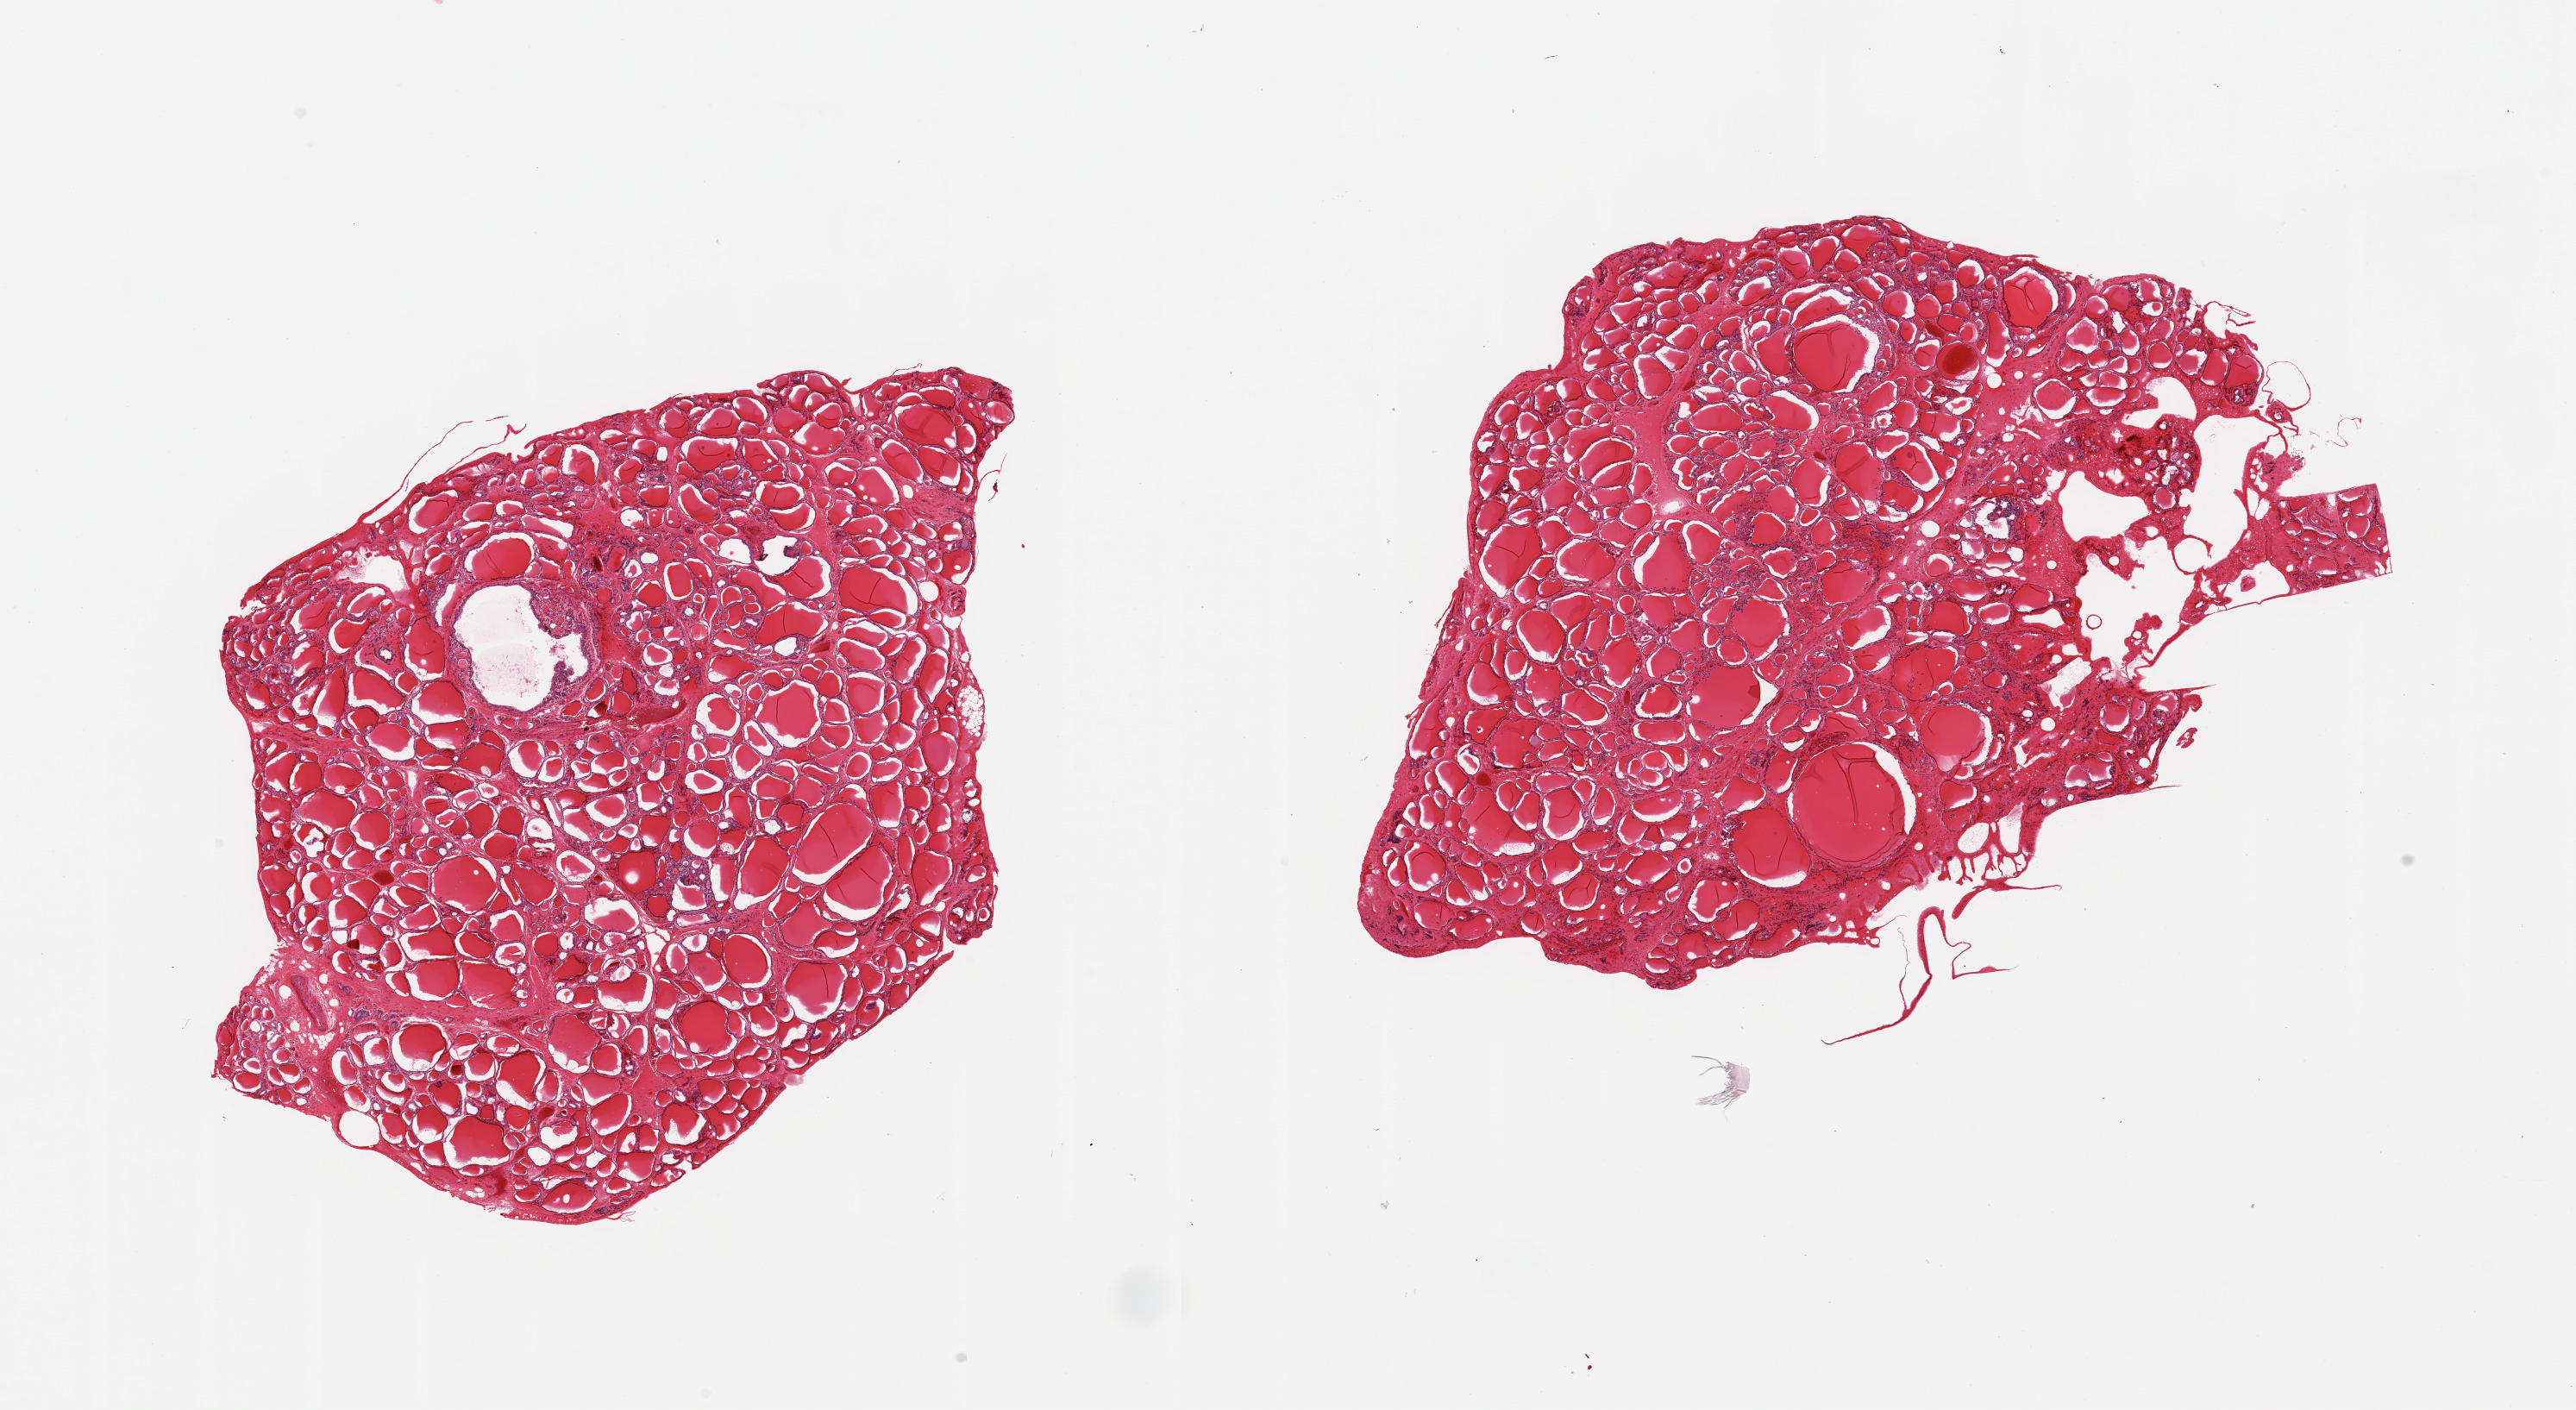
Whole-slide image, hematoxylin and eosin (H&E) stain — low-resolution overview of the scanned area, about 23.6 x 12.9 mm (slide scanned at 20x), PAXgene-fixed paraffin-embedded (PFPE) section, section of thyroid (target tissue), tissue donor sample. Male donor.
Pathologist's review note for this sample: 2 pieces, few minute (~1mm) colloid cysts.